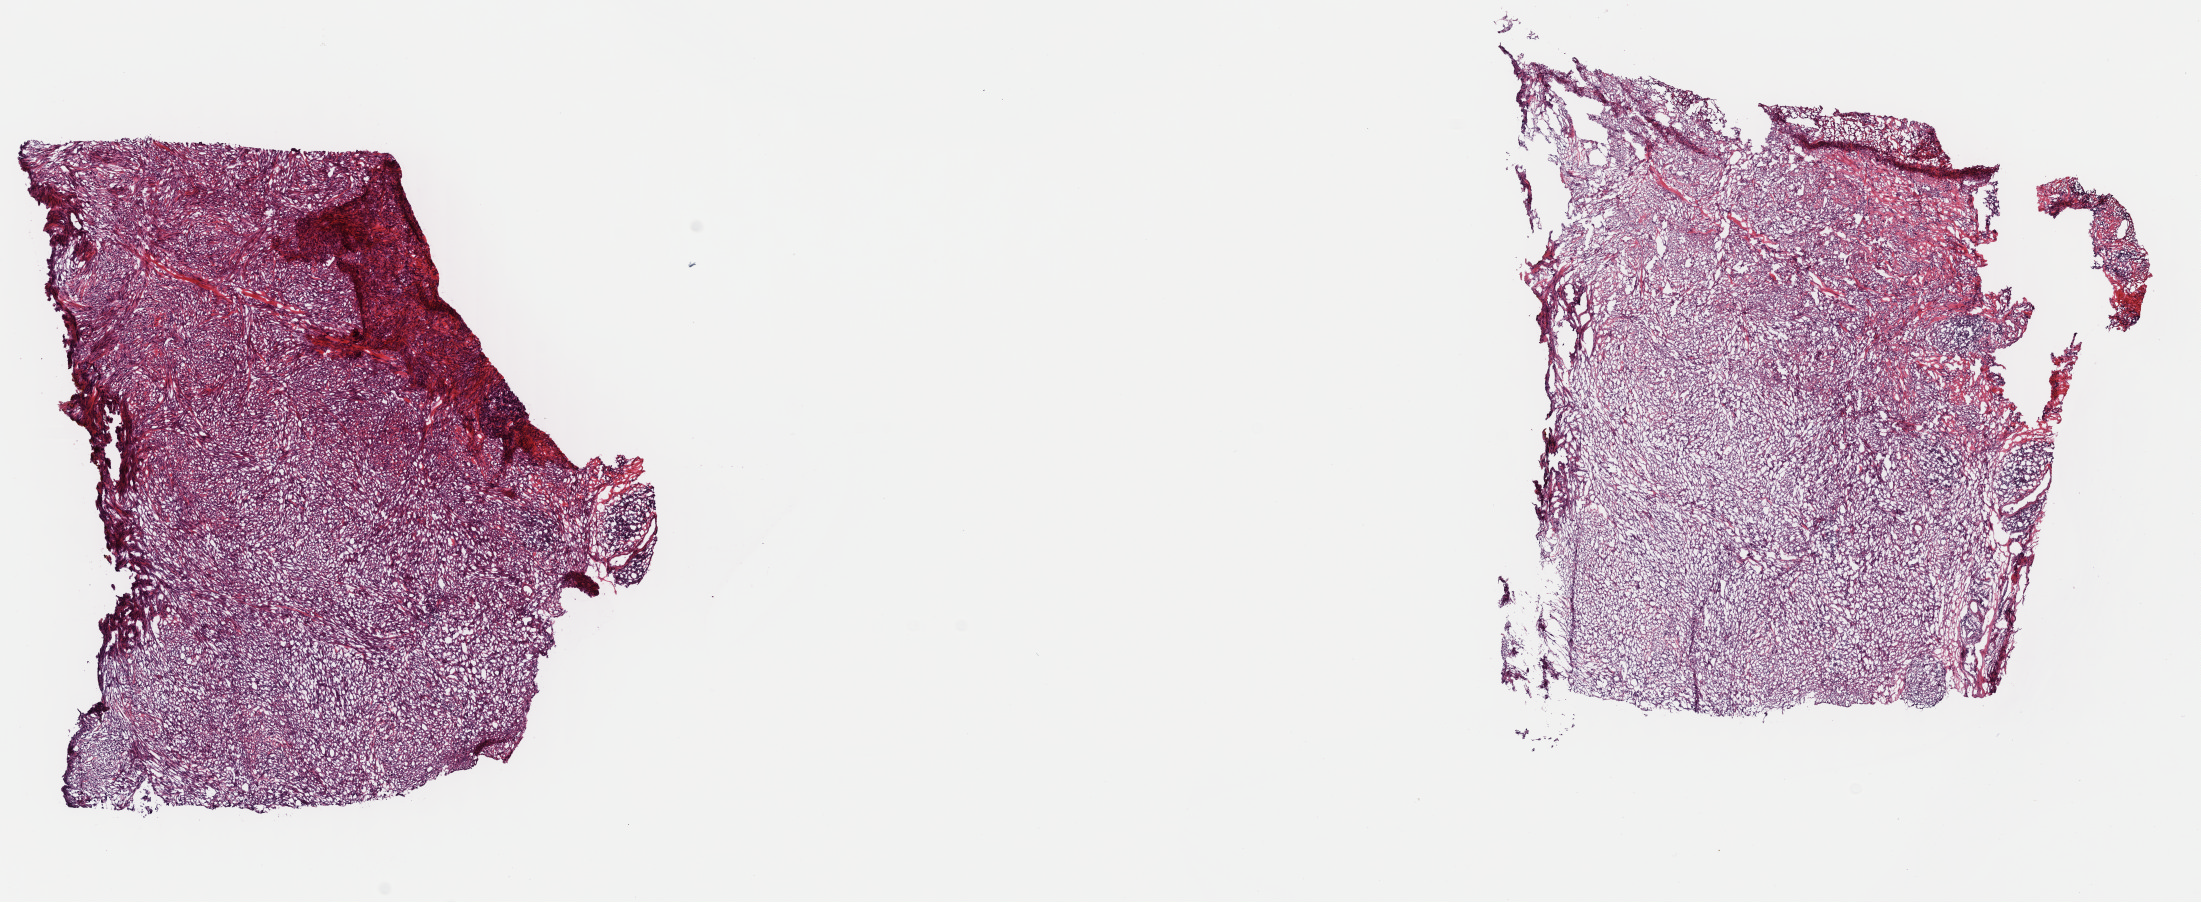
Whole-slide histology image, Hematoxylin and eosin (H&E) stained — shown as a low-resolution overview of the whole scanned area (about 17.4 x 7.1 mm, acquisition: 40x scan). Frozen section from the top of the tissue portion. Head and neck, primary tumour sample. Patient: male, age at initial diagnosis 43 years. Histologic grade: GX (grade cannot be assessed). Composition of this section per pathologist review: tumour cells 80%, tumour nuclei 80%, normal cells 0%, stromal cells 20%, necrosis 0%. Infiltration values recorded for this section: lymphocyte infiltration 10%, monocyte infiltration 0%, neutrophil infiltration 0%.
• histologic diagnosis: Squamous cell carcinoma, spindle cell (base of tongue, NOS)
• AJCC pathologic stage: IVA (7th edition)